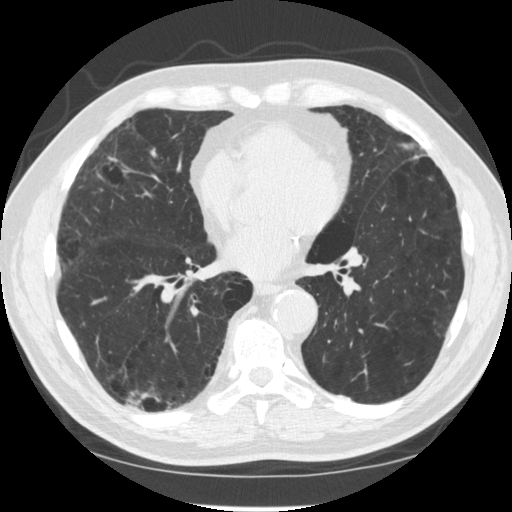
Low-dose screening chest CT, axial slice. Second annual screen. Lung window (W 1500 / L -600 HU). 1.25 mm slice thickness. Standard (soft-tissue) reconstruction kernel (STANDARD). Male, age 70 years at enrolment. Former smoker at enrolment.
Lesion marked by an expert reader, bounding box (x1, y1, x2, y2) in pixels: (120, 374, 171, 432). The screening reader recorded 2 non-calcified nodules or masses ≥4 mm on this exam (right lower lobe, right lower lobe); which of them this box marks is not recorded. Participant outcome: lung cancer diagnosed 617 days after this screen (after the third annual screen) — squamous cell carcinoma, NOS, right upper lobe, poorly differentiated (G3), stage IV (AJCC 6th edition).